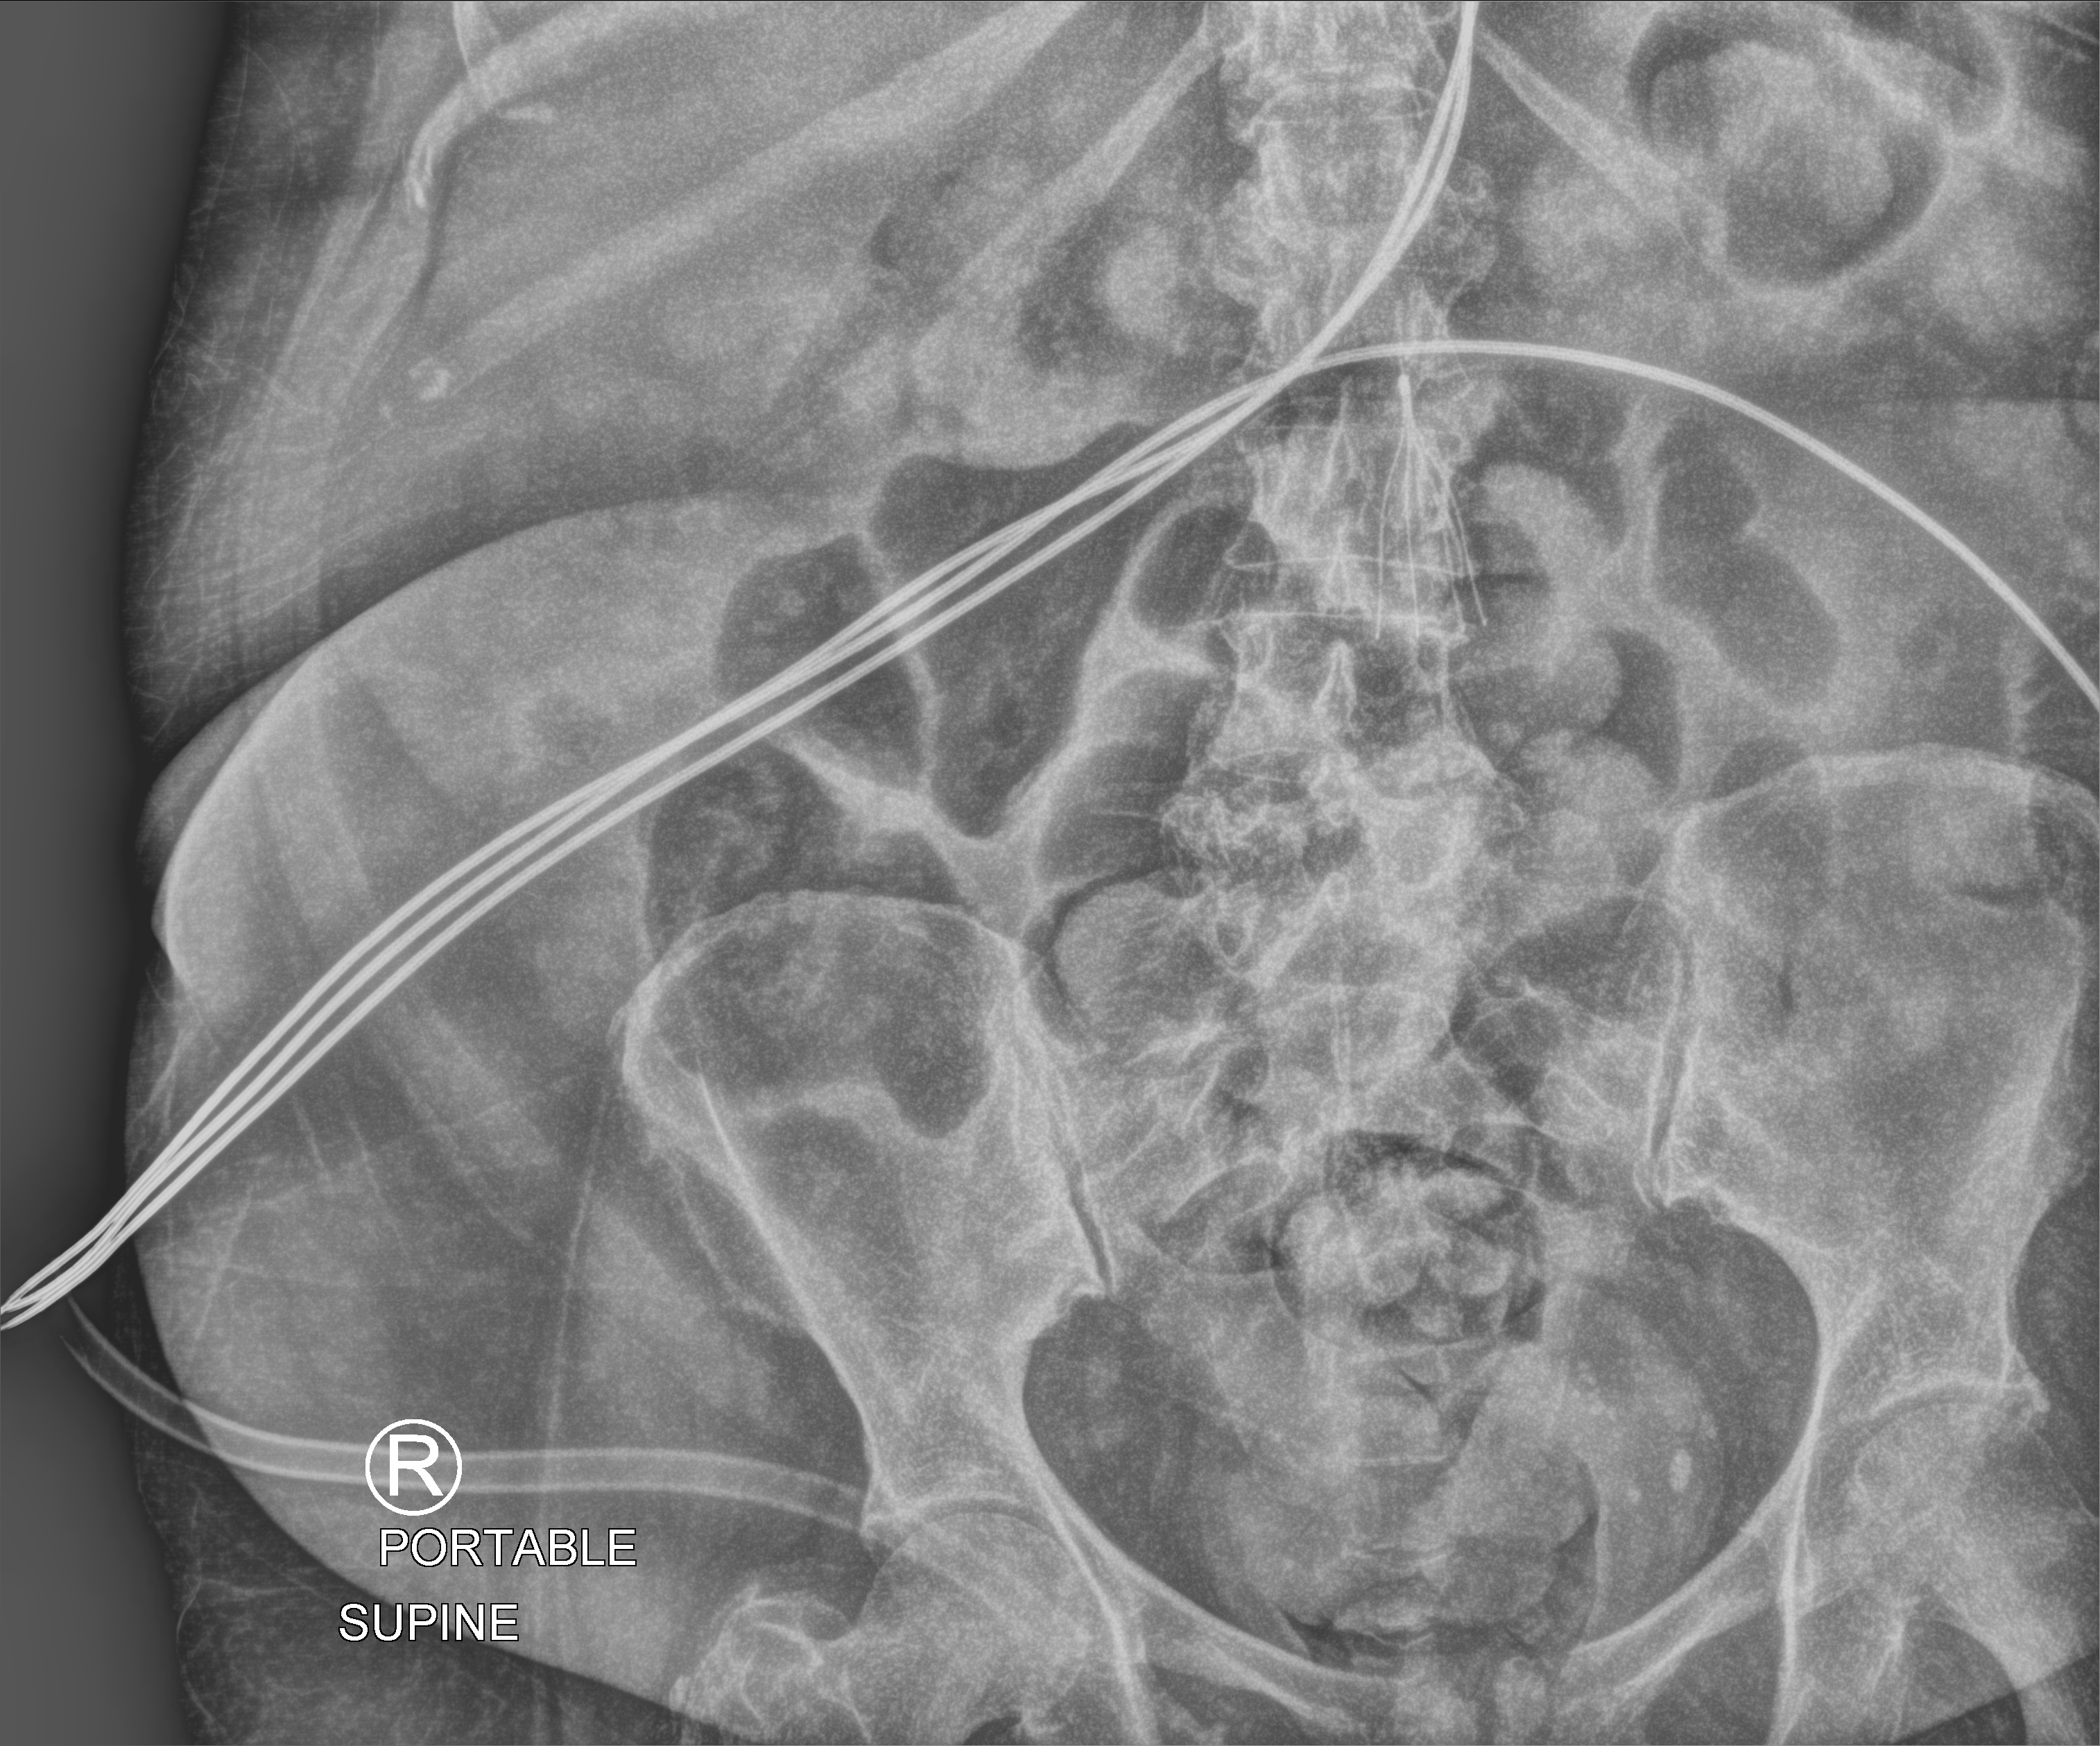
Abdomen X-ray (portable); anteroposterior (AP) projection. Female patient hospitalised with COVID-19, age 60–74 years.
Admission-level facts for this patient (not findings on this image; timing relative to this image not recorded): mechanically ventilated during this hospital stay: no.